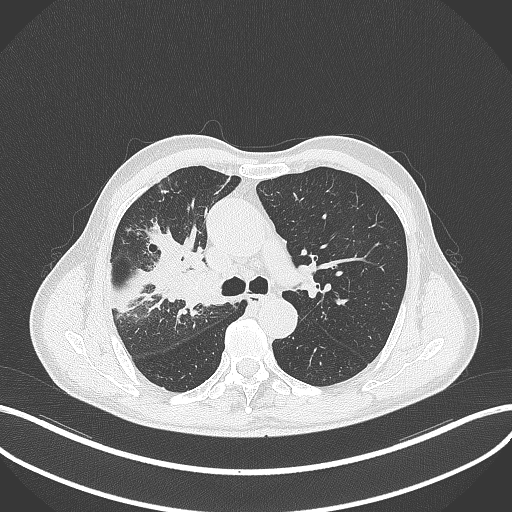
Chest CT, one axial slice; slice 320 of 490 in the series (ordered by position); reconstruction kernel B70f; 120 kVp; lung window (W 1500 / L -600 HU); 512 × 512 image matrix. Patient: male, 69 years. From the clinical record (not read from this slice): clinical TNM (as recorded): T2a N0 M0.
Structures marked on this image (rectangle marked by the reading radiologist):
- lung tumour (recorded histology: adenocarcinoma): bounding box (x1, y1, x2, y2) in pixels: (169, 257, 229, 314)